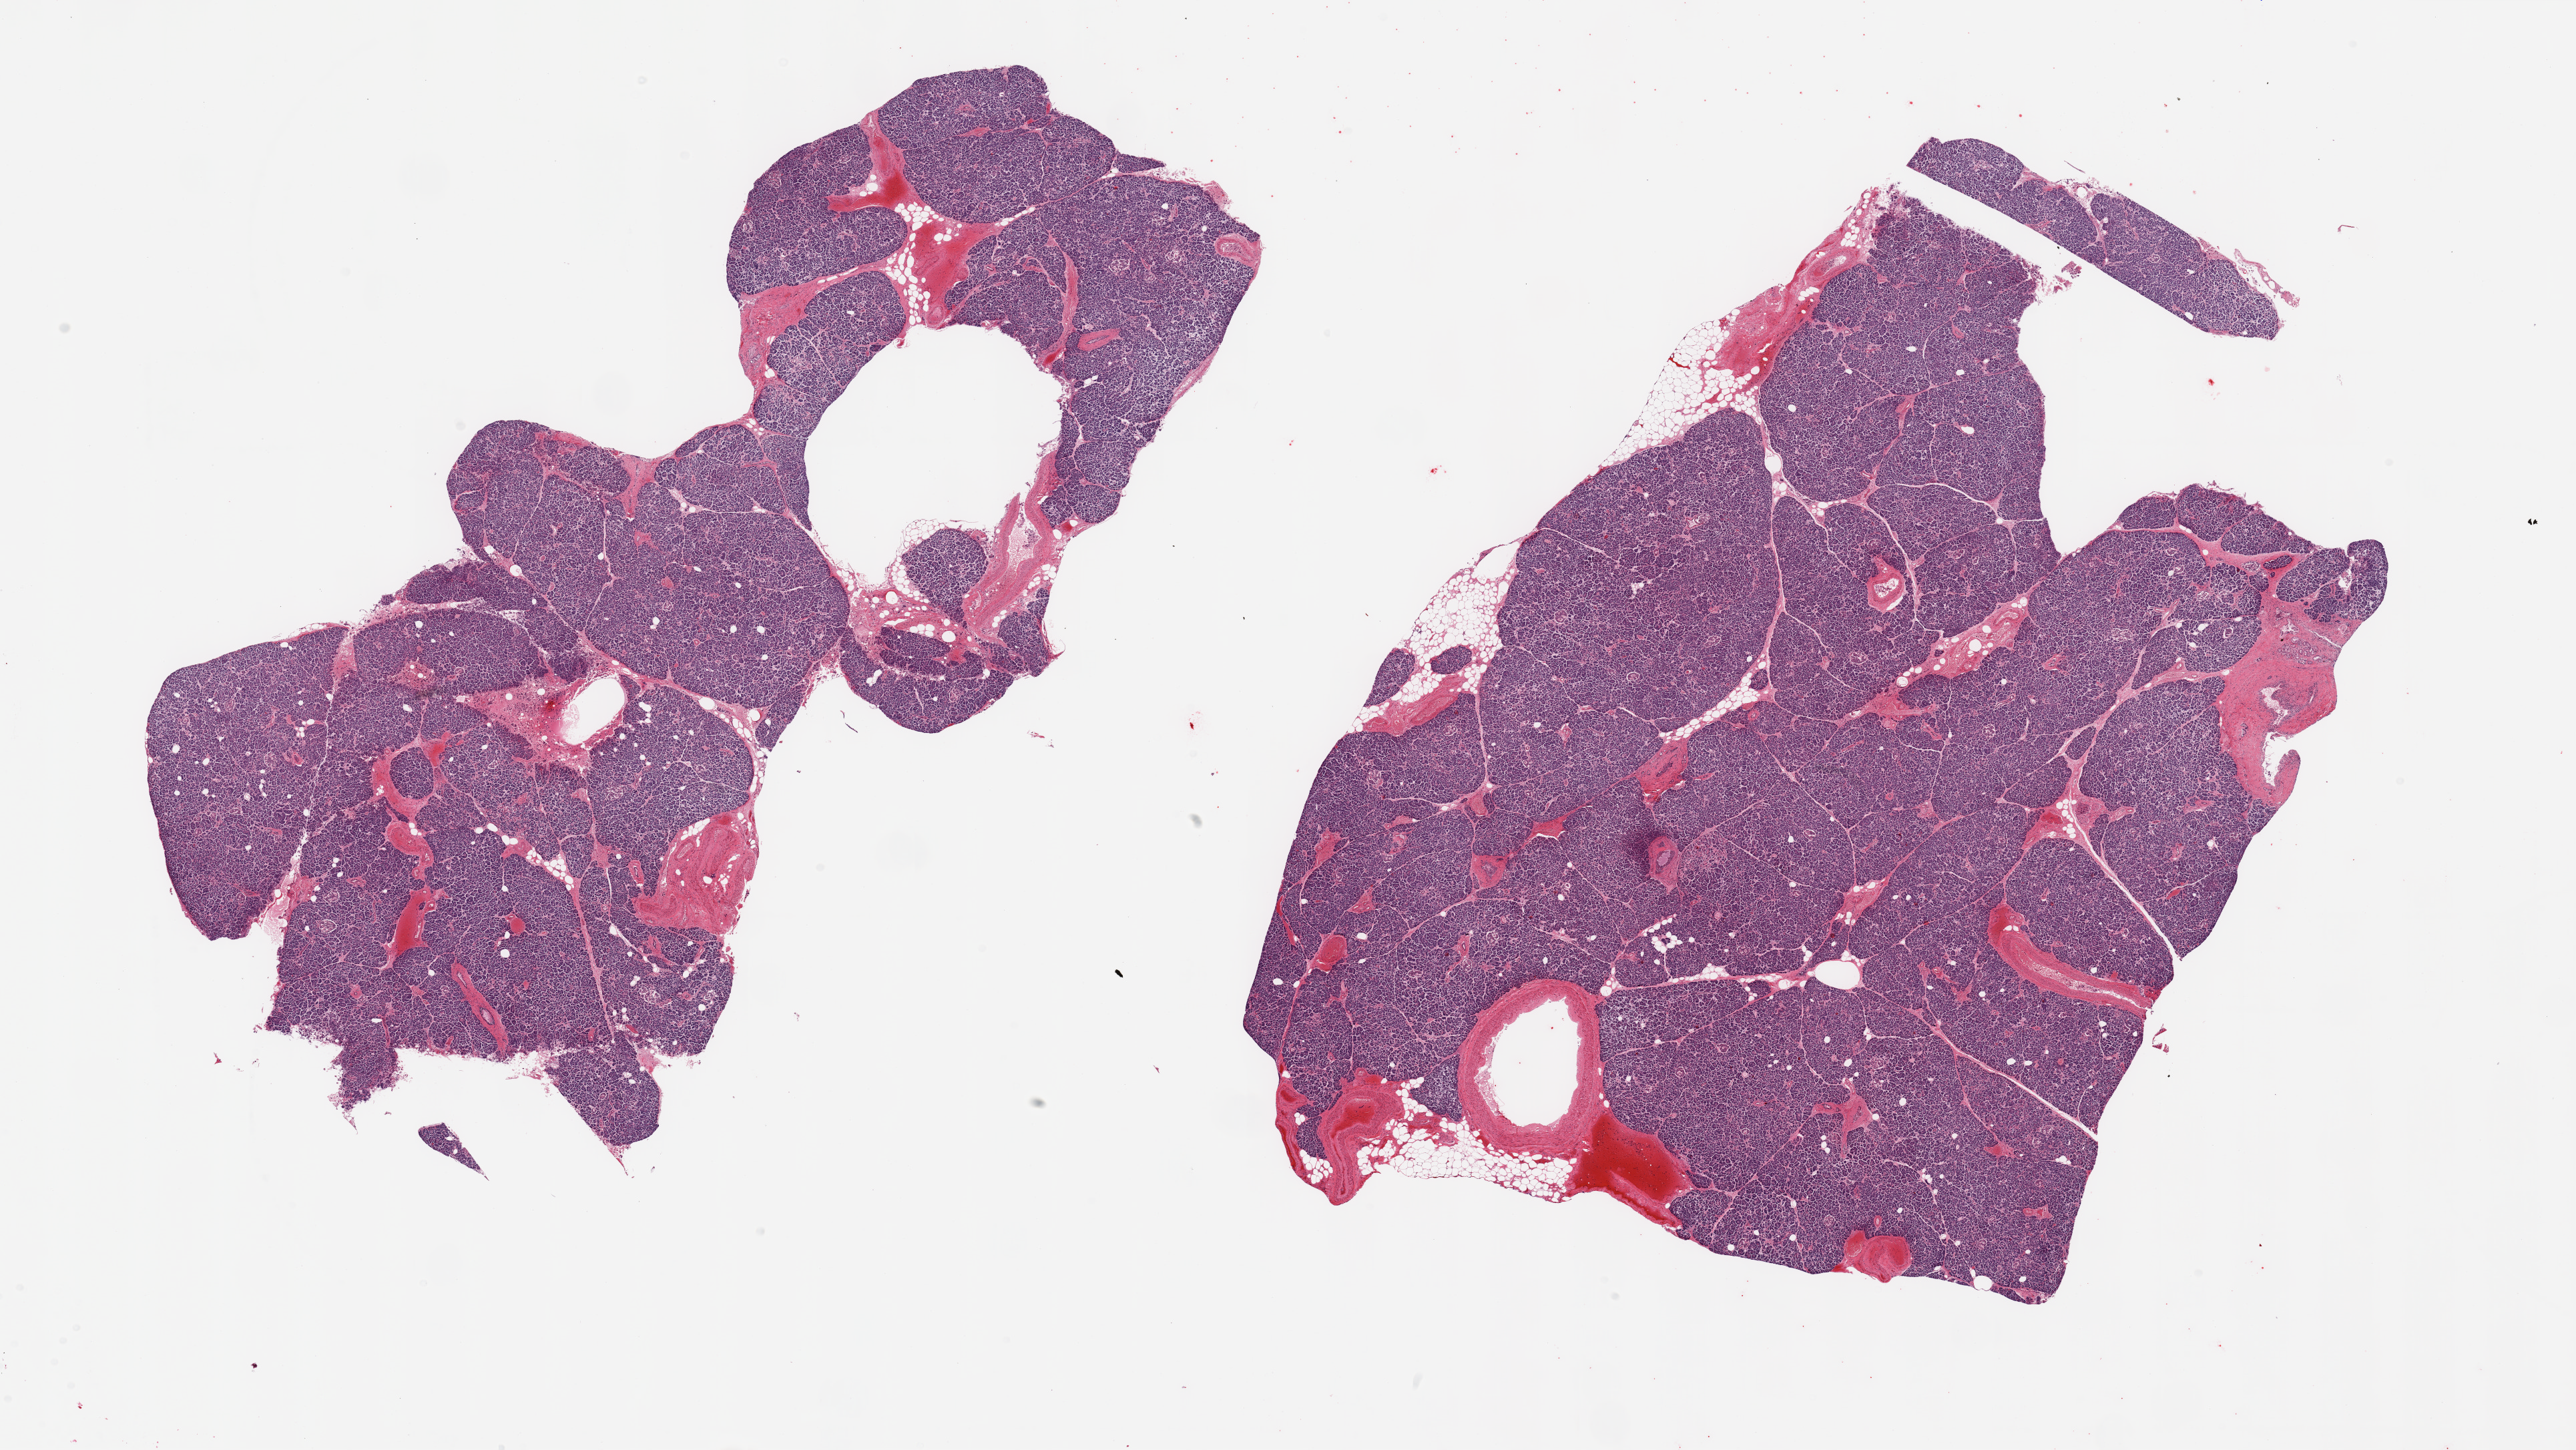
Whole-slide image, hematoxylin and eosin (H&E) stain — shown as a low-resolution overview of the whole scanned area (about 30.5 x 17.2 mm). PAXgene-fixed paraffin-embedded (PFPE) section. Target tissue: pancreas. Tissue donor sample. Donor sex: male.
- review note (as recorded): 2 pieces